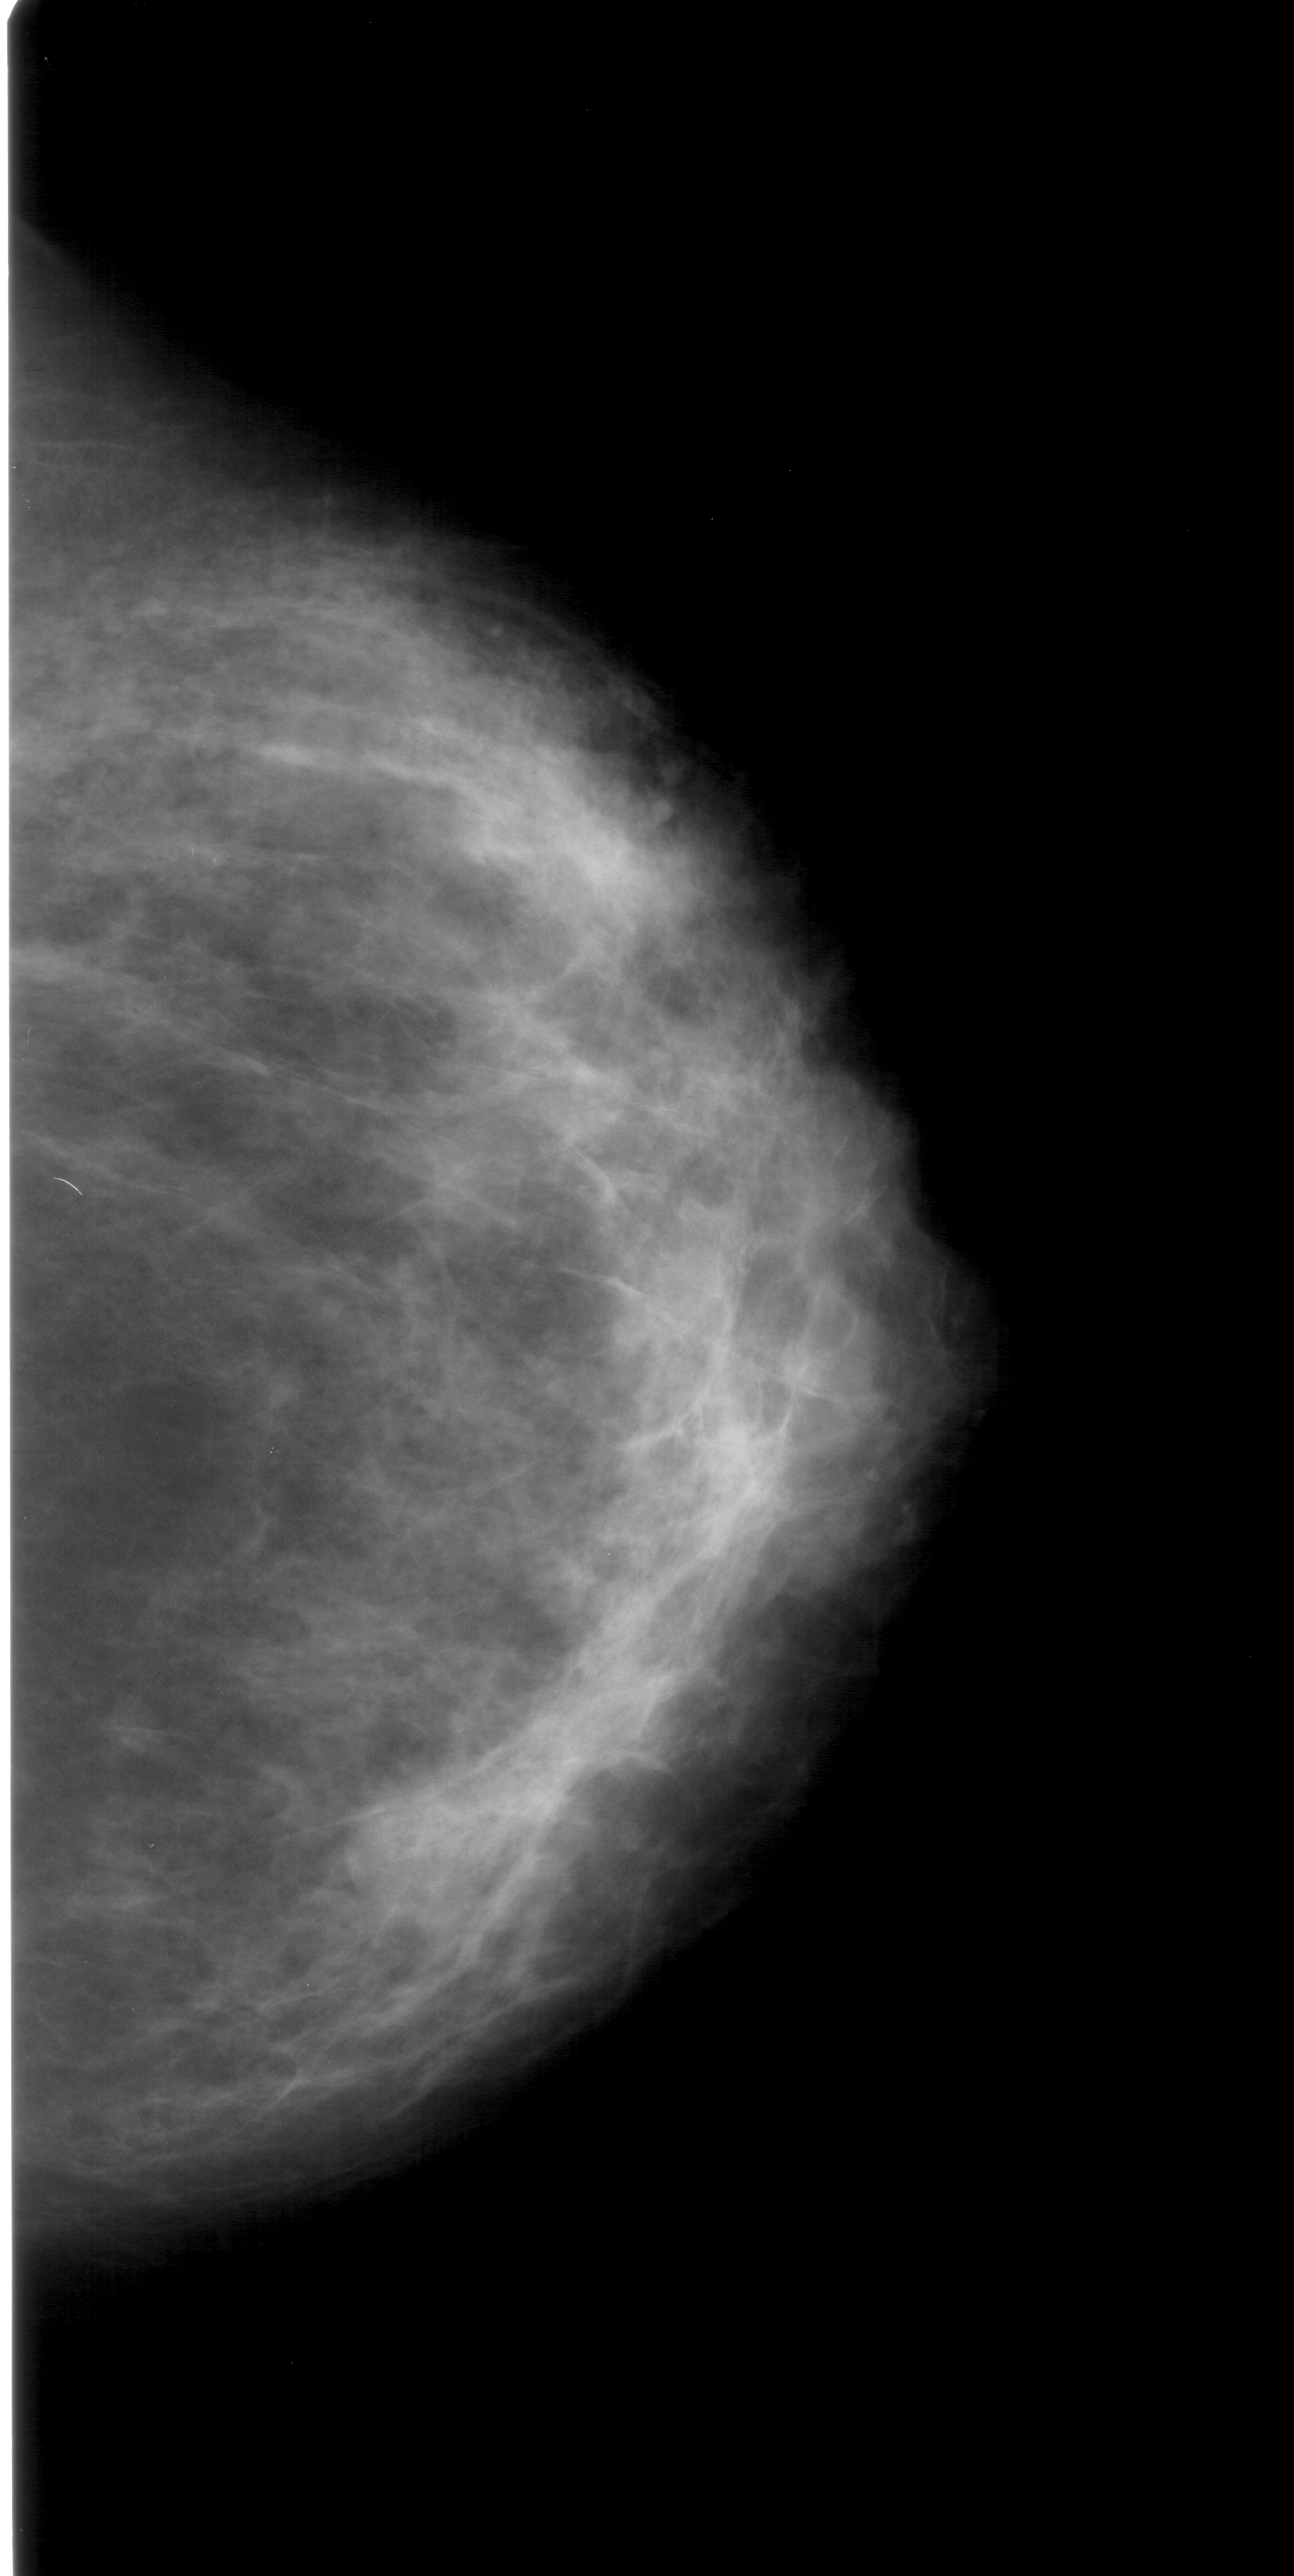
Mammogram (digitized film), right breast, CC view, breast composition: heterogeneously dense (BI-RADS density category 3 of 4).
Mass, shape round, margins obscured; BI-RADS assessment category 4; pathology (as recorded): benign.